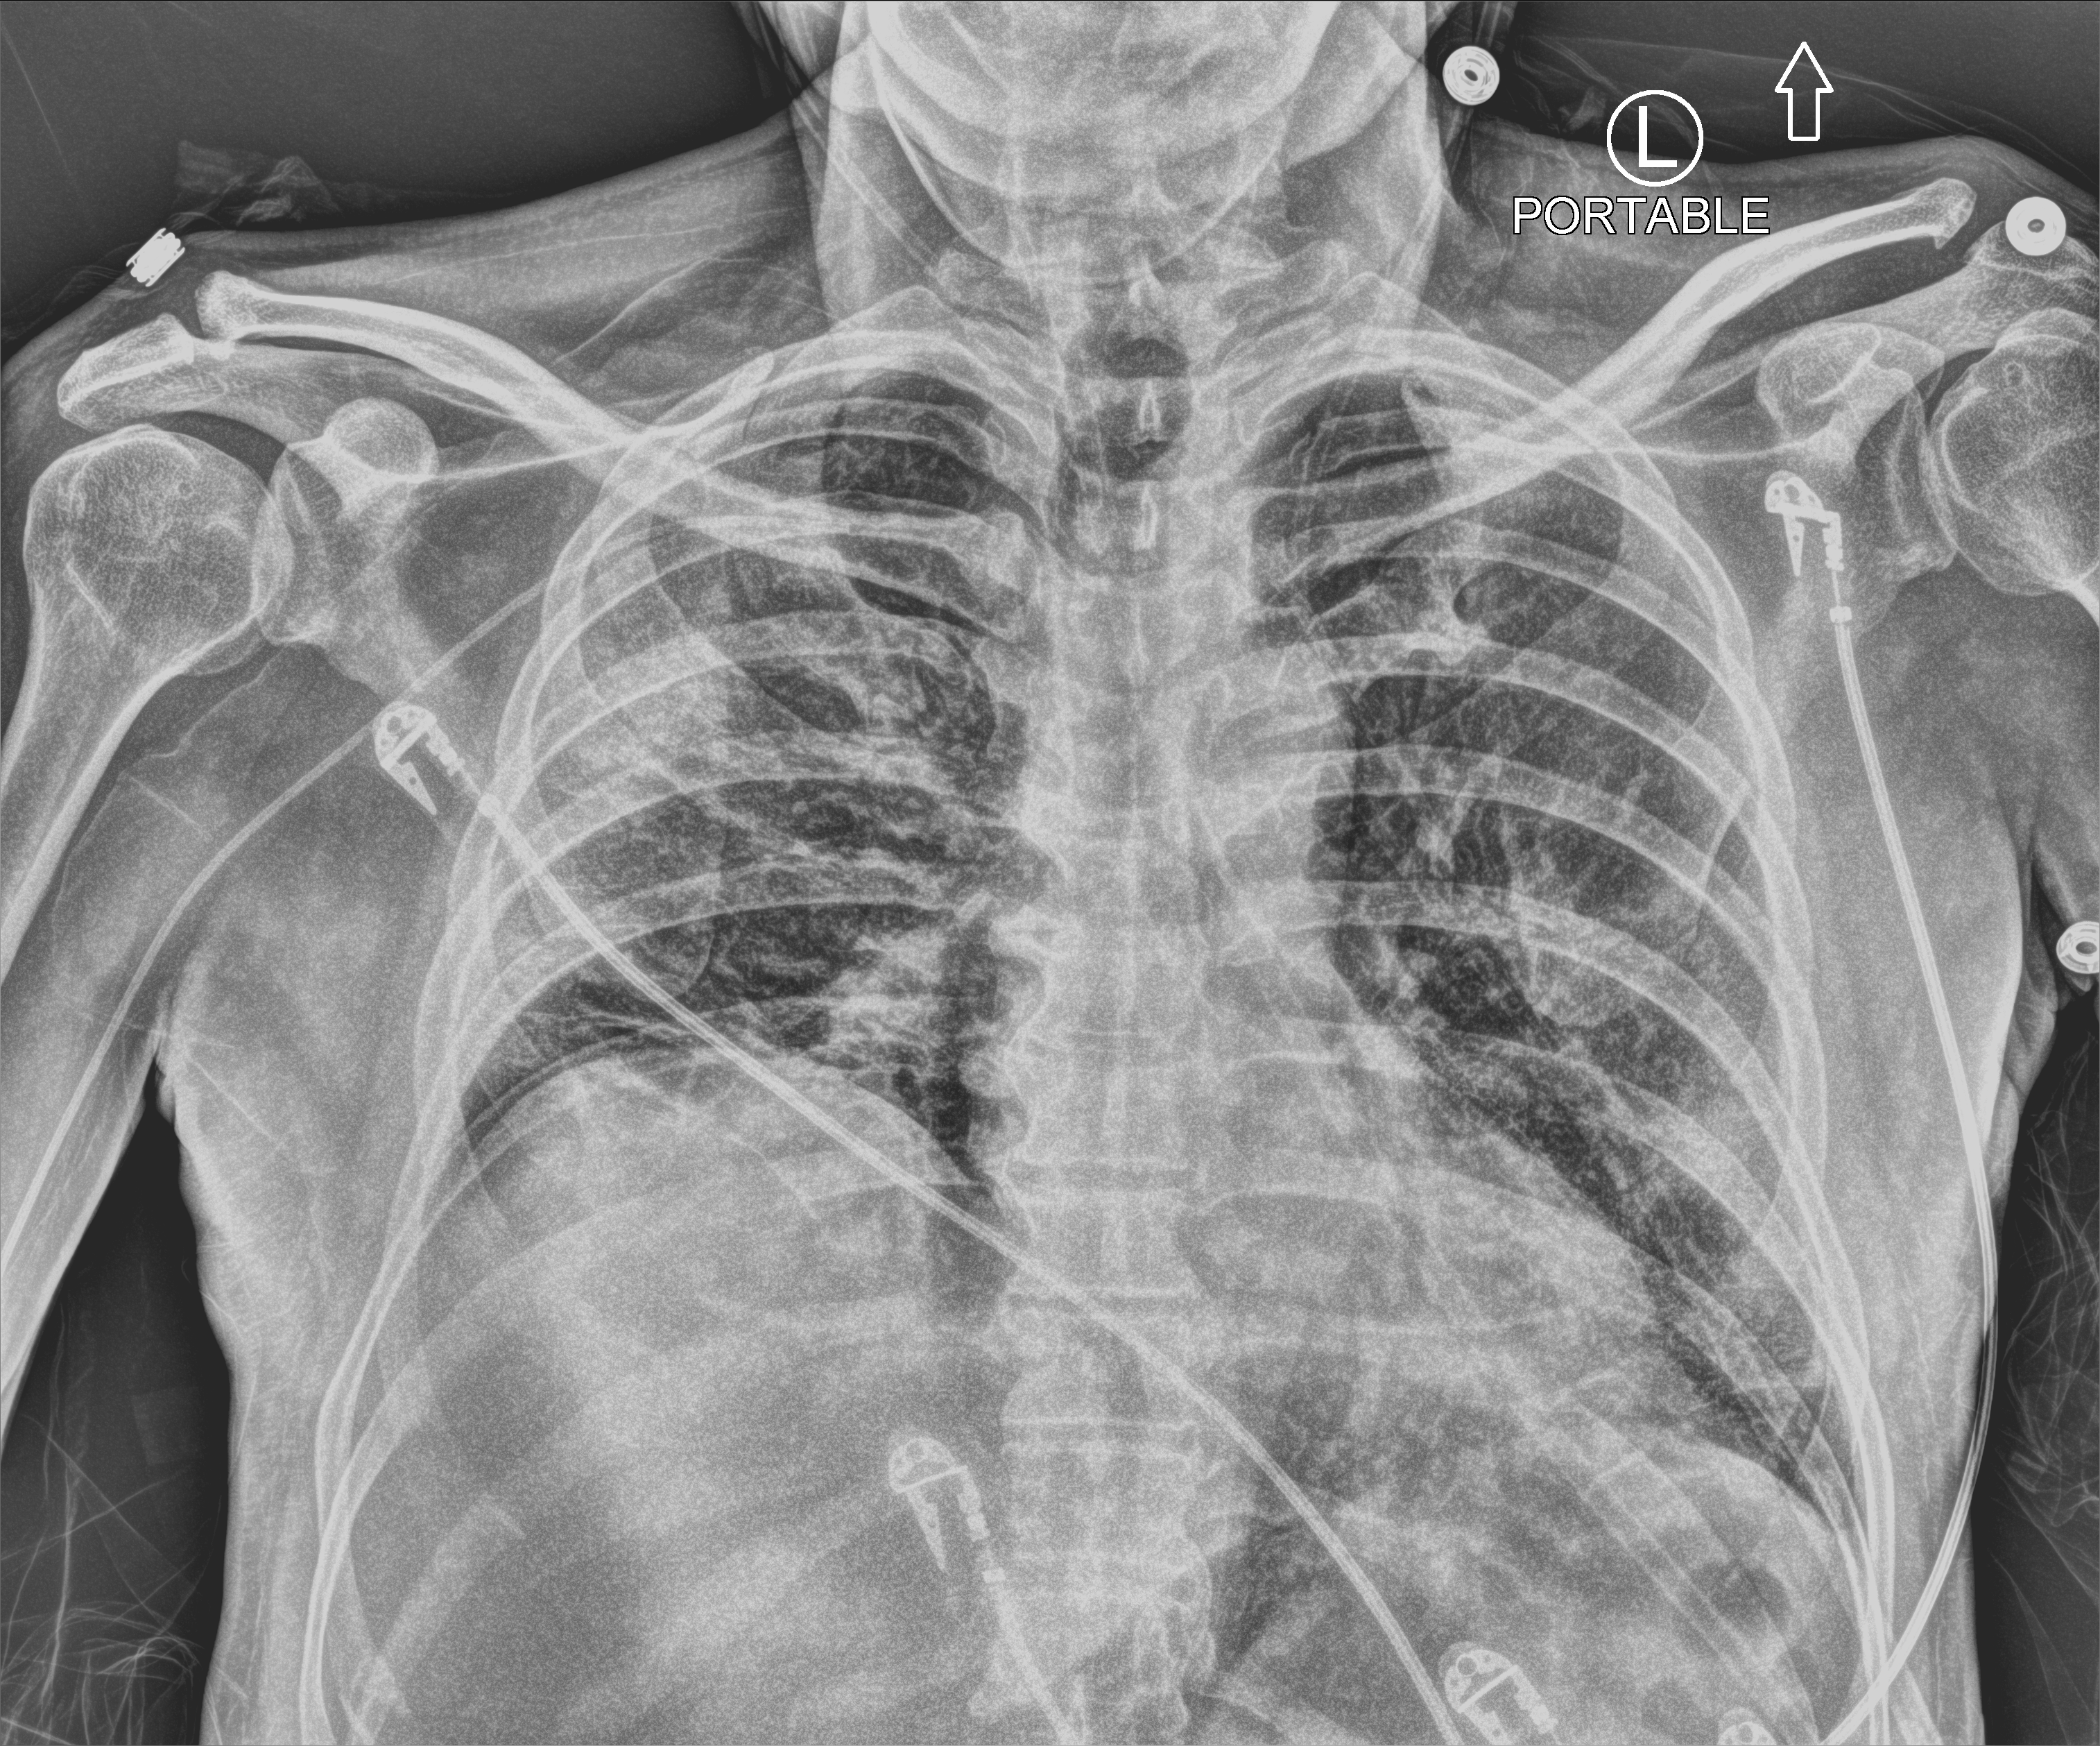
Portable chest radiograph, anteroposterior (AP) projection. Patient hospitalised with COVID-19; male, aged 60–74 years.
From the hospital-stay record, not from the radiograph (when in the stay this image was taken is not recorded): mechanically ventilated during this hospital stay: no.